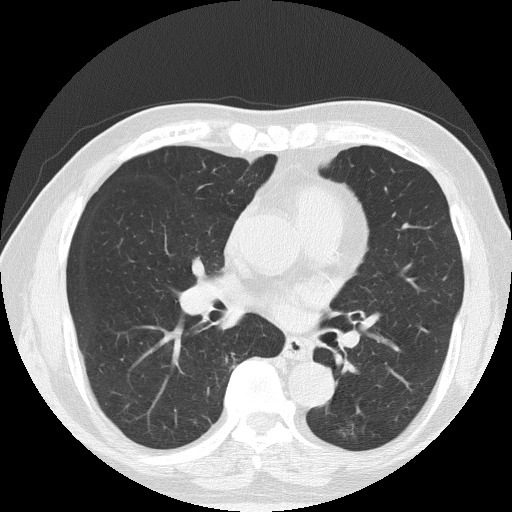
Chest CT (low-dose screening protocol), one axial image; baseline screening round; lung window (W 1500 / L -600 HU); 2 mm slice thickness; lung (sharp) reconstruction kernel (FC51); slice 79 of 145 in the series. Male, age 71 years at enrolment. Former smoker at enrolment.
- Expert reader's lesion annotation, box from (x=322, y=407) to (x=371, y=451) px.
- No non-calcified nodule or mass ≥4 mm was recorded by the screening reader at this exam.